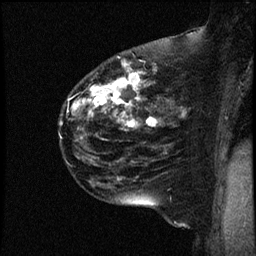
Breast MRI (dynamic contrast-enhanced), one sagittal slice. Position 34 of 44 along the scan axis. Dynamic contrast-enhanced study with each time point stored as its own series, time point 2 of 4 at this slice position (early post-contrast, ordered by acquisition time). 1.5 T. TE 4.2 ms, TR 17.7 ms. 2 mm slice thickness. 256 × 256 image matrix. Patient: female, 52 years. Case-level facts recorded for this patient, not image findings: setting: breast cancer imaged before/during neoadjuvant chemotherapy; receptor status: HR-positive, HER2-negative.
Annotated regions visible in this slice (semi-automatically segmented with operator editing):
- analysis volume of interest (the breast-tissue region the enhancement analysis was run in; not a lesion): bounding box (x1, y1, x2, y2) in pixels: (58, 48, 163, 147)
- tumour enhancement mask (voxels above the 100 % enhancement threshold inside the analysis volume of interest): (60, 63, 158, 128)